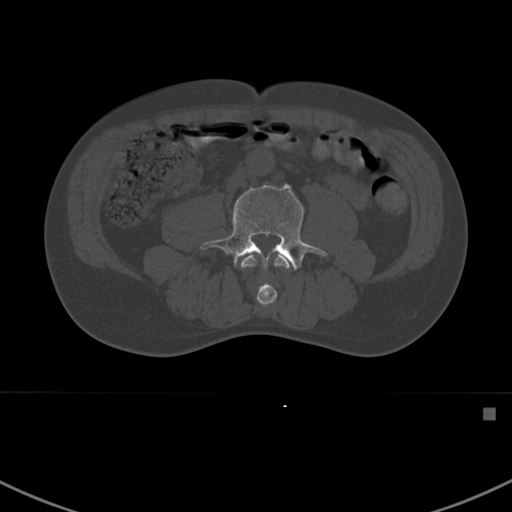
CT including the spine, one axial slice. Slice 247 of 412 in the series (ordered by position). Bone window (W 1800 / L 400 HU). 1.5 mm slice thickness. 512 × 512 image matrix, field of view 358 × 358 mm. Male patient, age 59 years. From the clinical record (not read from this slice): primary cancer: prostate.
Outlined on this slice (semi-automatic segmentation, software-assisted and operator-edited):
- L3 vertebra: box from (x=240, y=254) to (x=294, y=307) px
- L4 vertebra: (x=200, y=183)–(x=327, y=270)